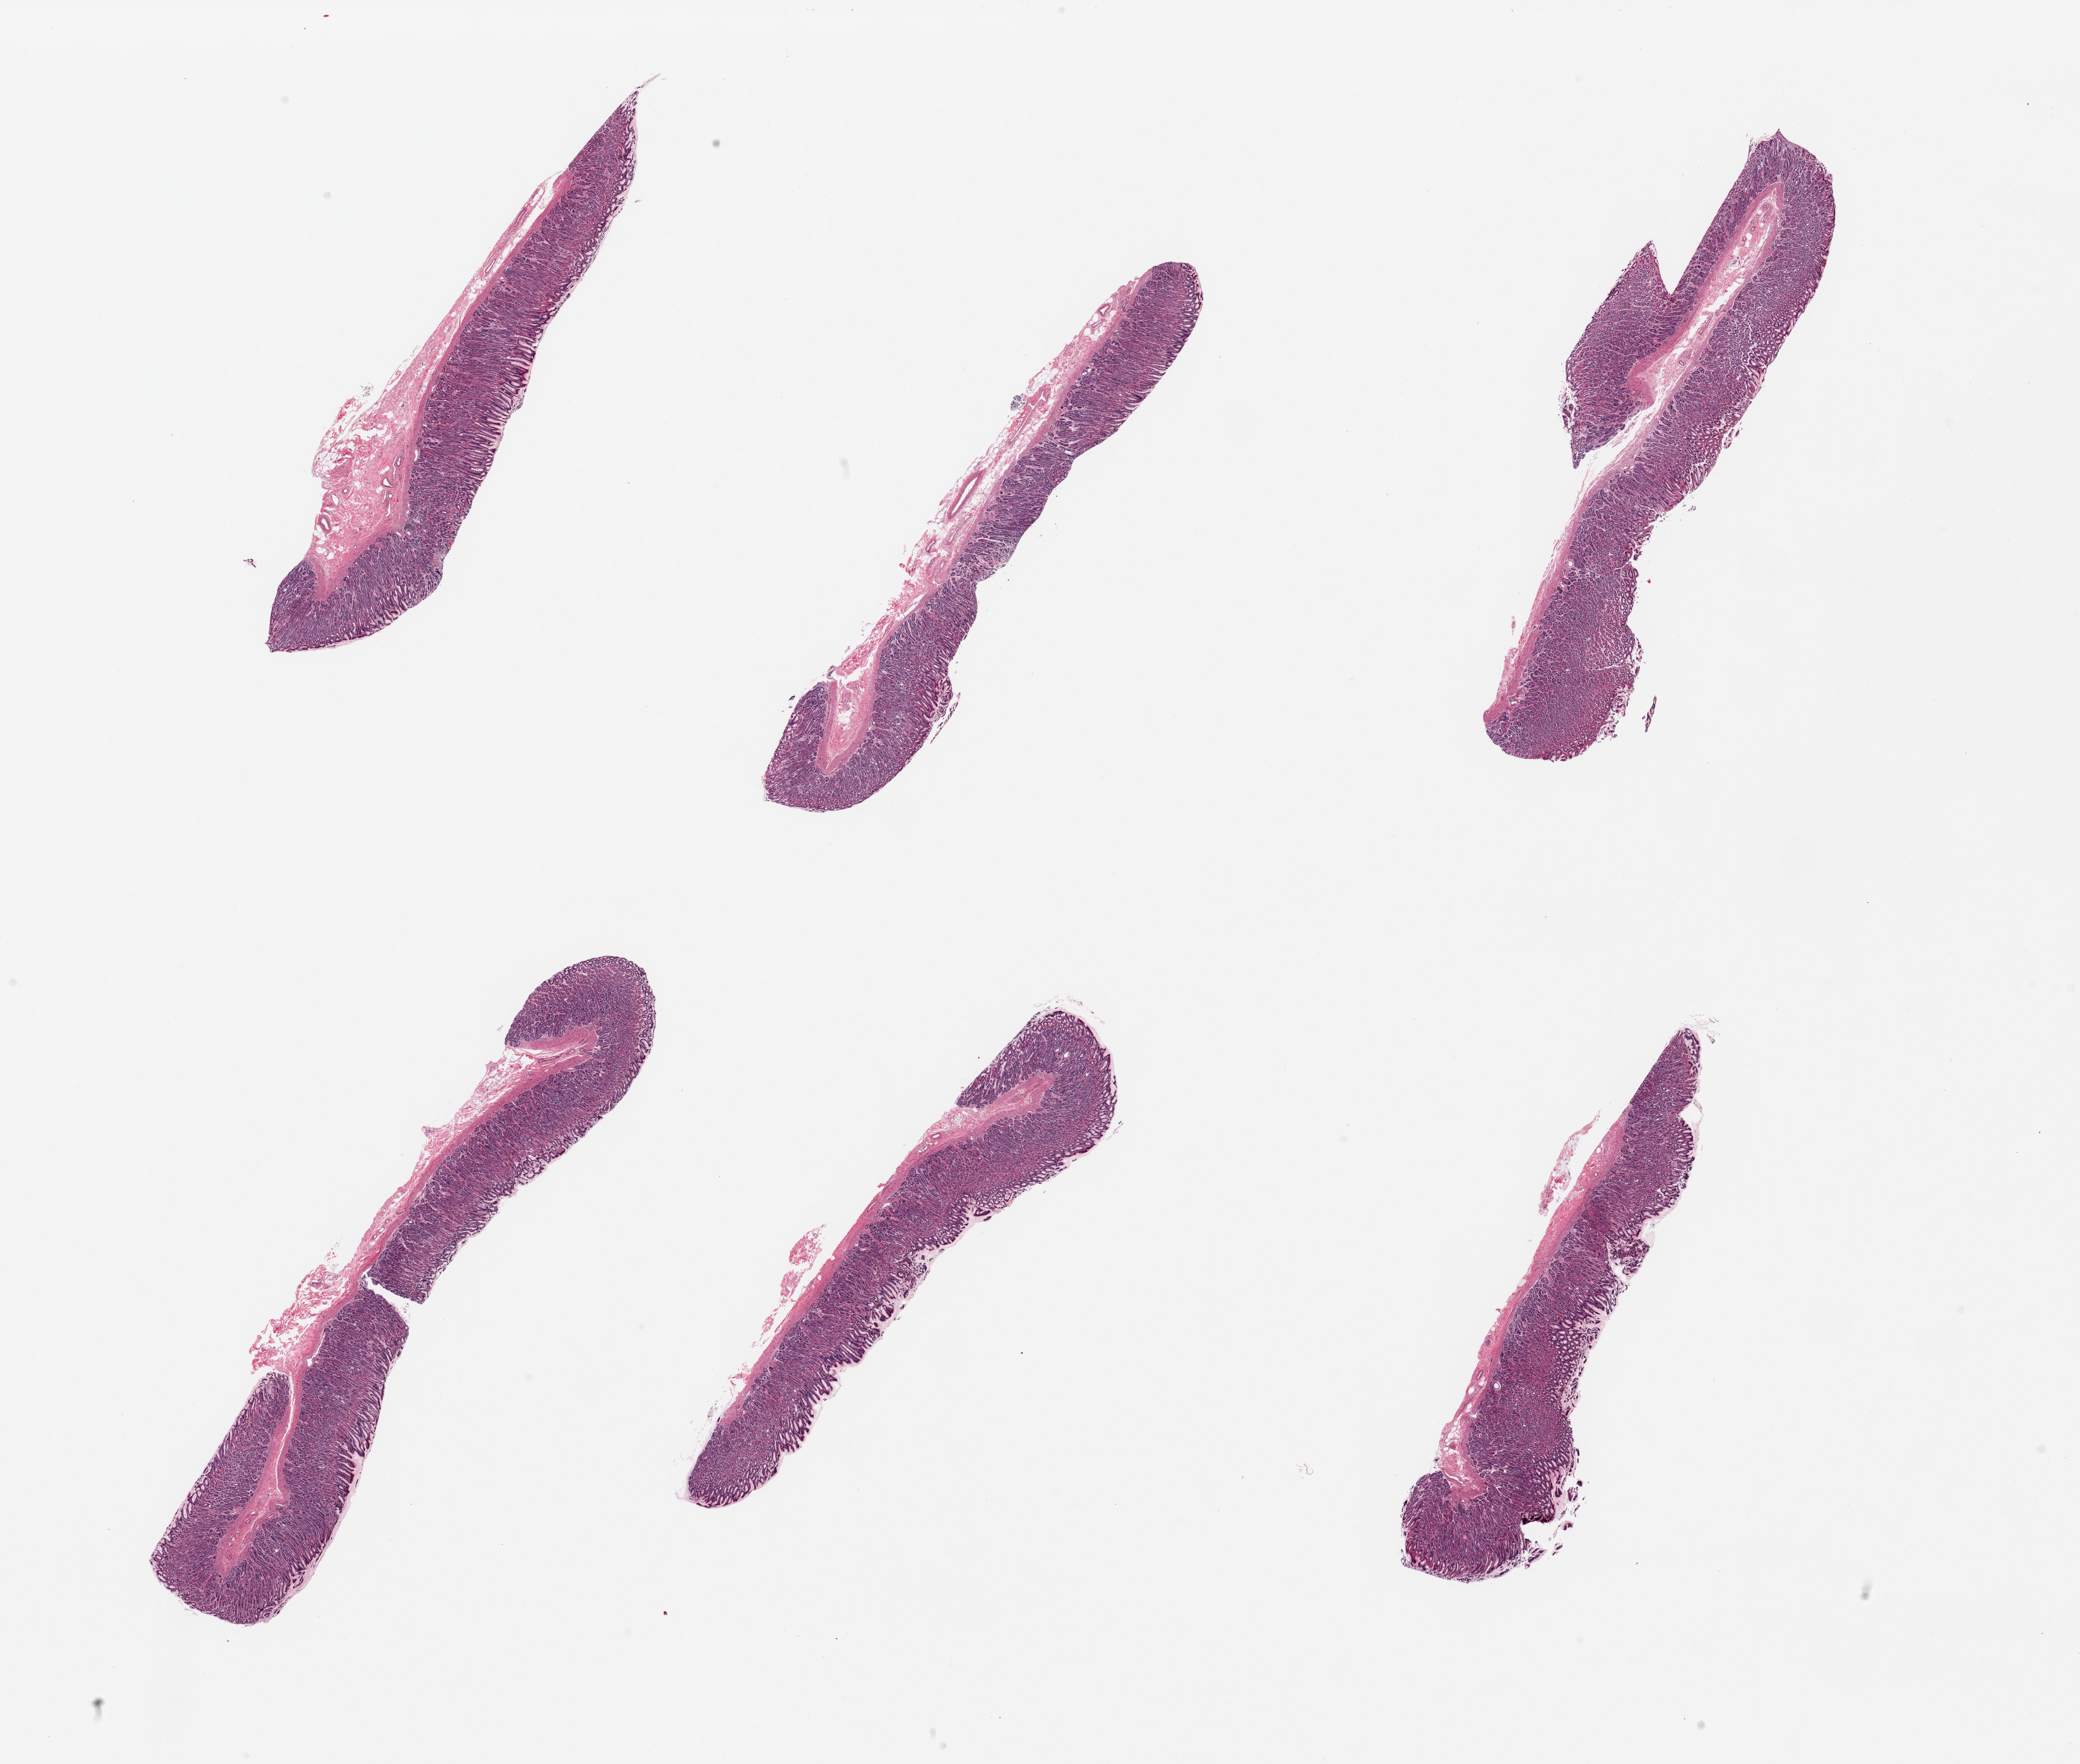
Hematoxylin and eosin (H&E) whole-slide image, brightfield, whole scanned area (about 25.6 x 21.7 mm, from a 20x scan) shown as a low-resolution overview. PAXgene-fixed paraffin-embedded (PFPE) section. Section of stomach (target tissue). Donor tissue sample. Donor sex: female.
Review note (as recorded): 6 pieces, well preserved mucosa is 60-90% thickness, good specimen.